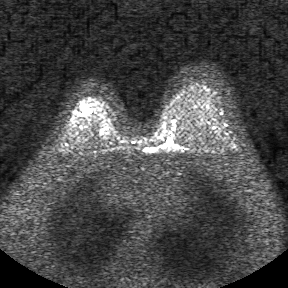
Breast MRI, one axial slice; slice 28 of 34 in the series (ordered by position); diffusion-weighted series; image 2 of 4 stored at this slice position (different b-values; order by instance number); 1.5 T; 5 mm slice thickness; 288 × 288 image matrix, field of view 340 × 340 mm. Female patient.
Structures marked on this image (expert manual segmentation):
- tumour on diffusion-weighted imaging: bounding box (x1, y1, x2, y2) in pixels: (83, 108, 91, 113)